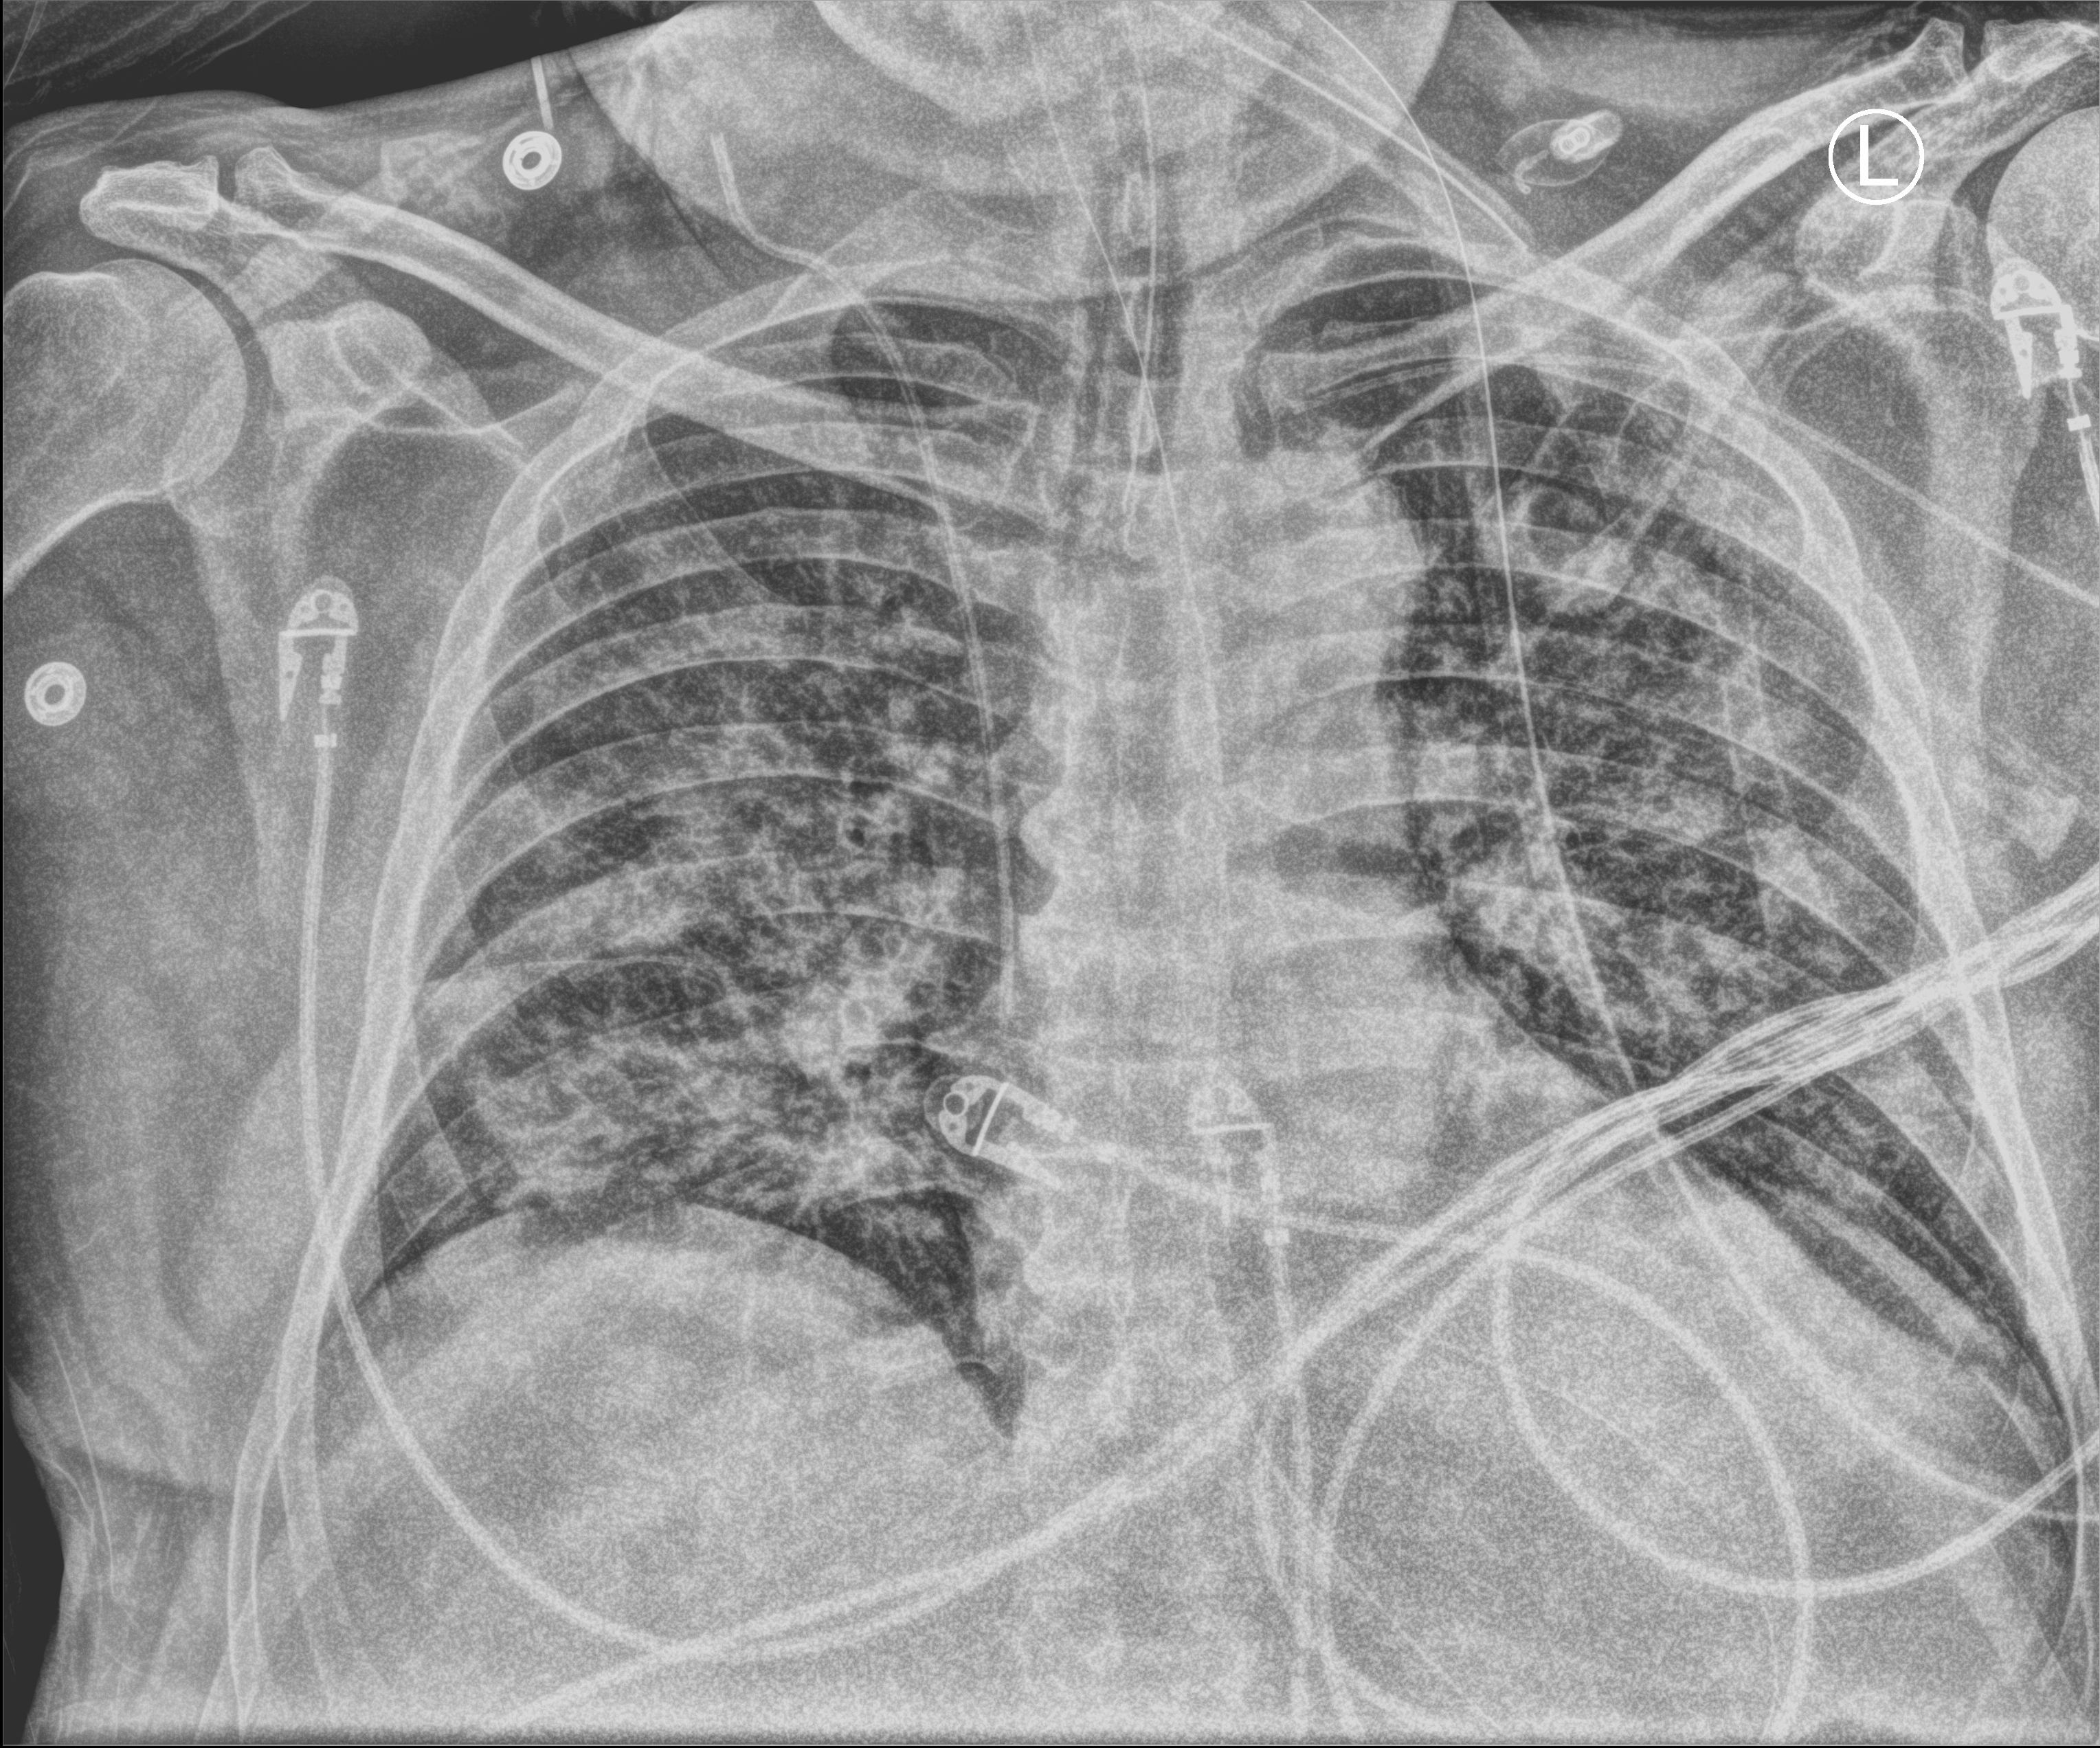
Portable chest radiograph. Male patient hospitalised with COVID-19, age 60–74 years.
Hospital-stay facts (about this admission, not read from this image; timing relative to this image not recorded):
- mechanically ventilated during this hospital stay: yes
- admitted to intensive care during this hospital stay: yes
- chronic kidney disease (admission record): no